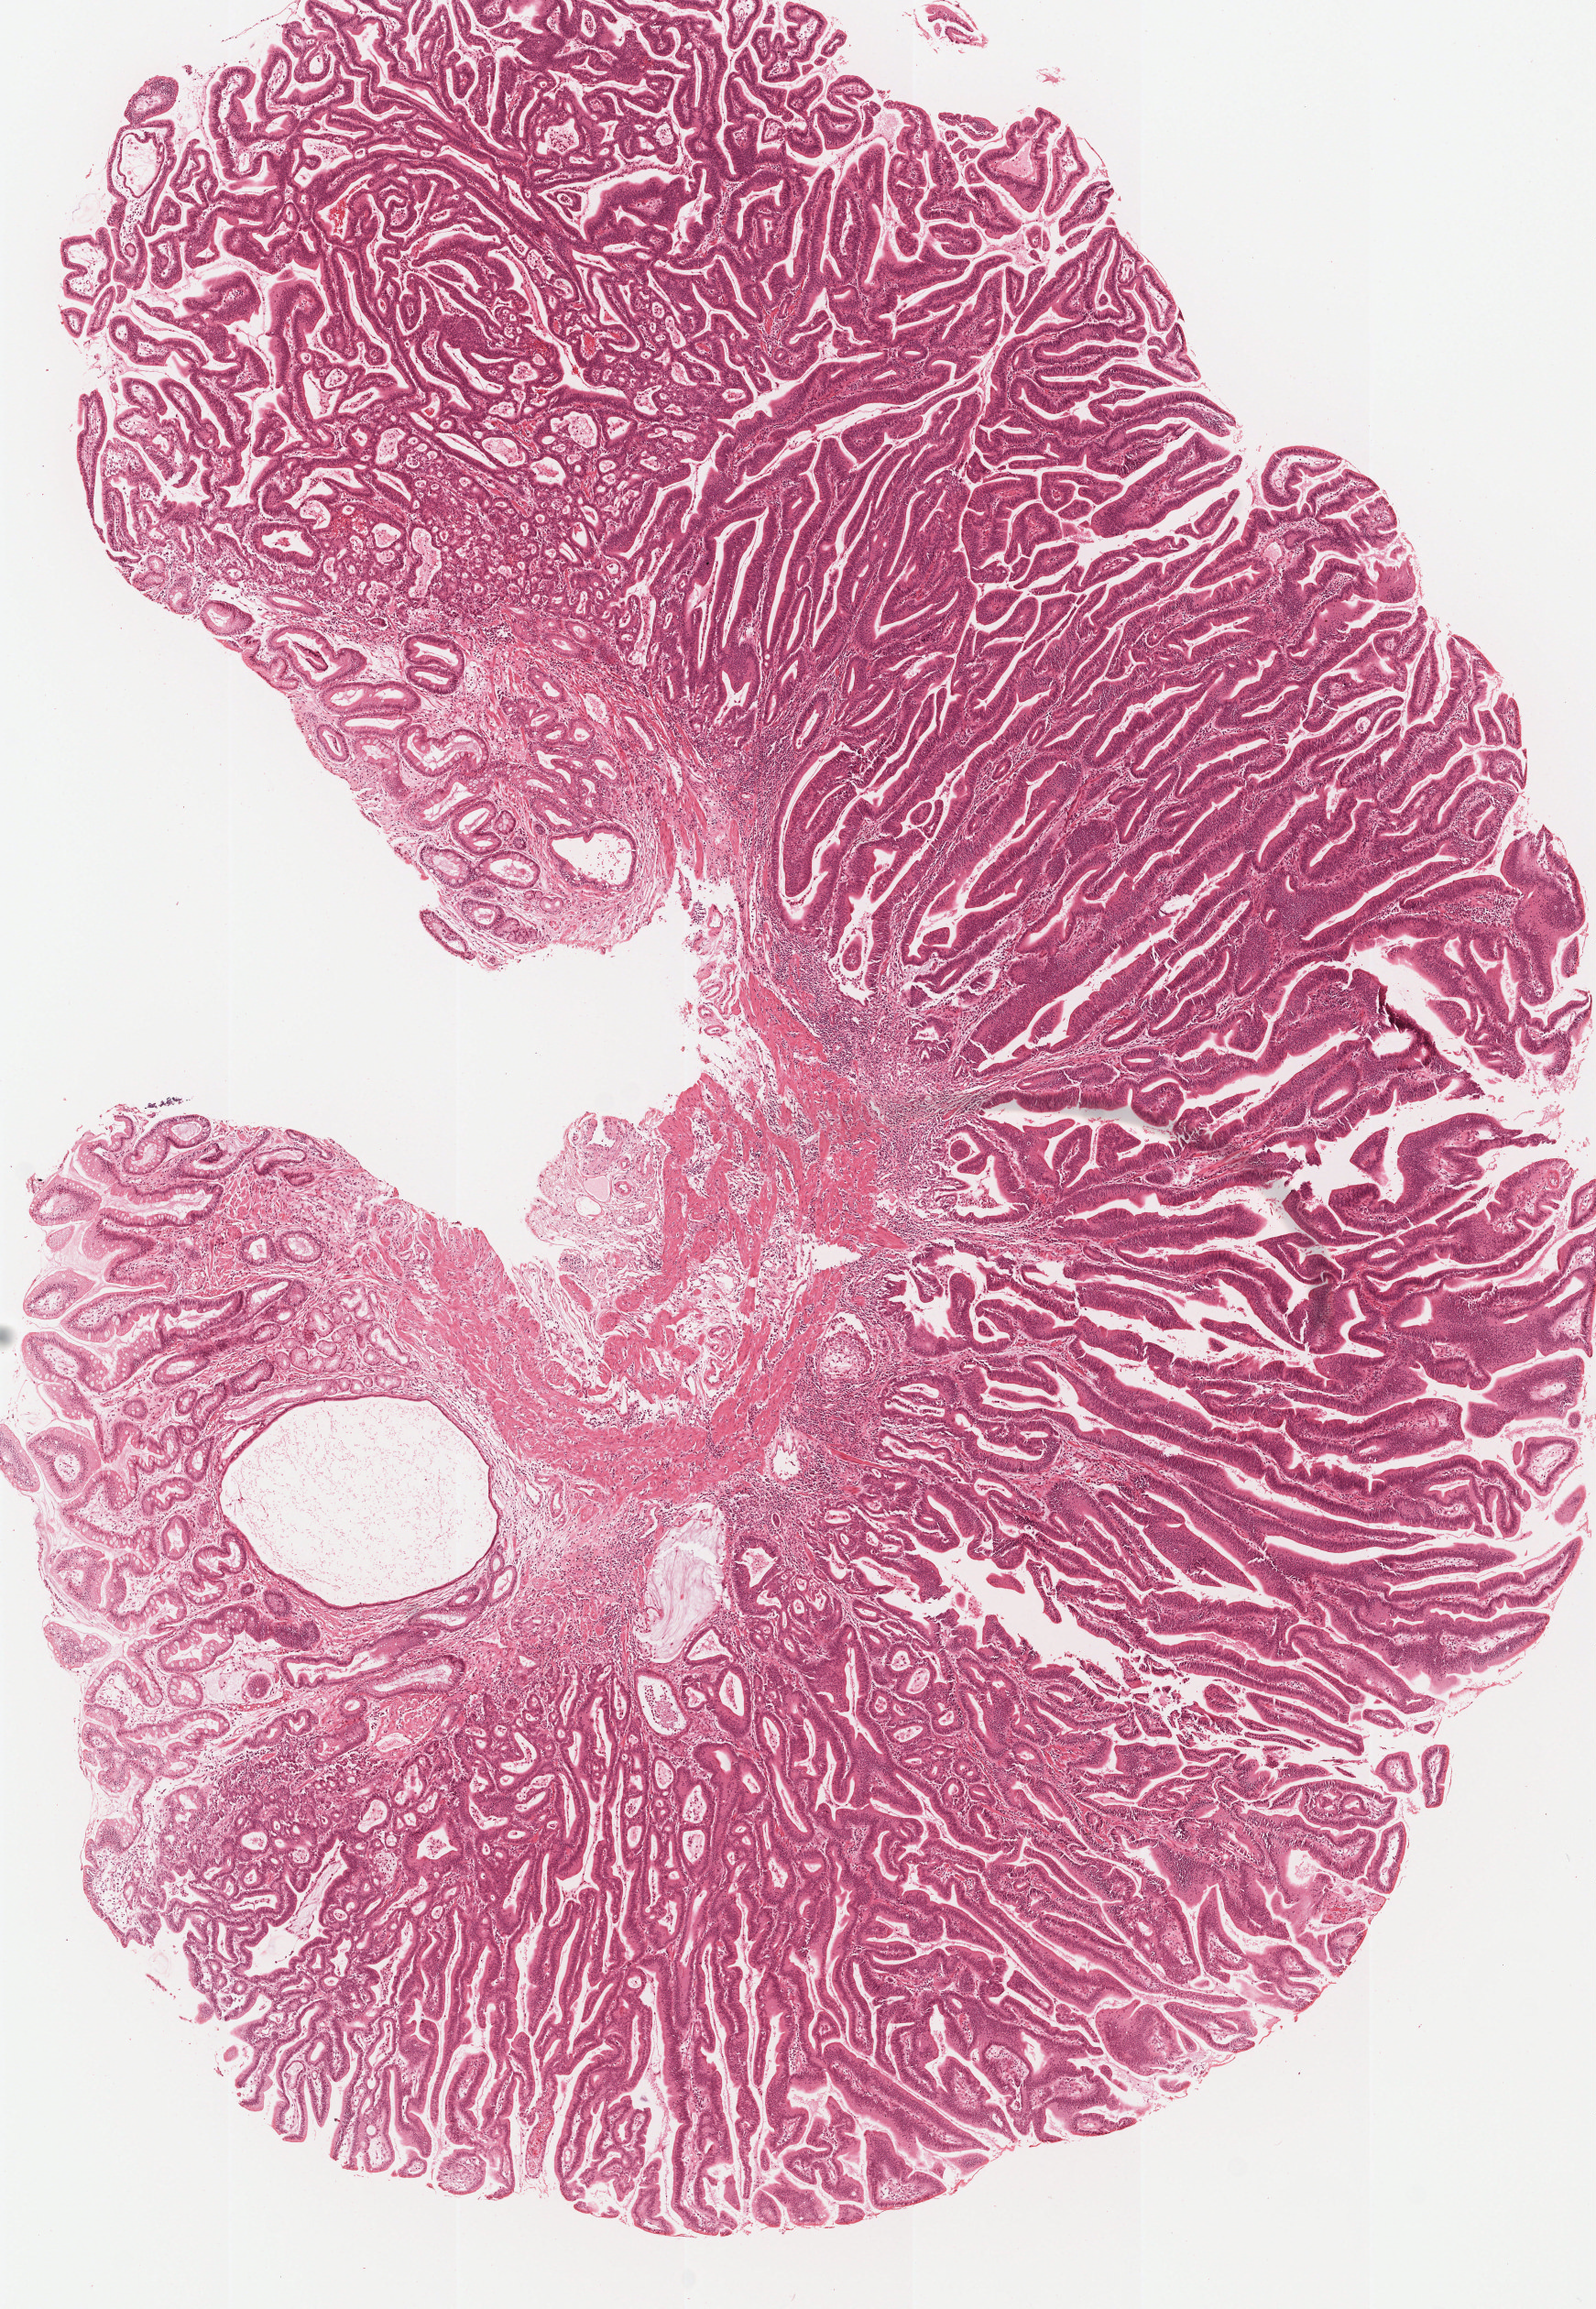
Whole-slide histology image, H&E, a low-resolution overview of the entire scanned area, about 6.9 x 10.0 mm (slide scanned at 20x), formalin-fixed paraffin-embedded (FFPE) diagnostic section, stomach, primary tumour sample. Male patient; age at initial diagnosis 77 years.
Pathologic diagnosis: Tubular adenocarcinoma (gastric antrum).